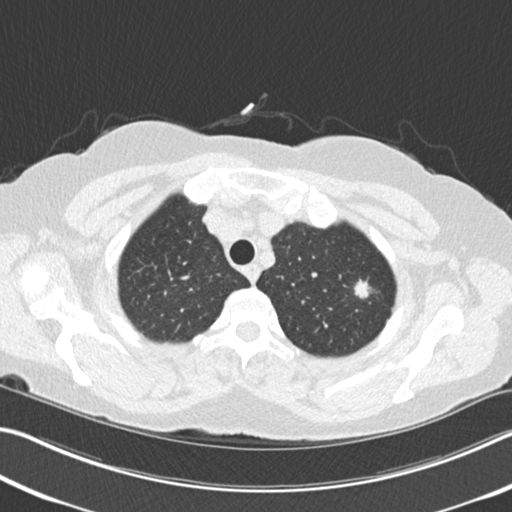
Chest CT (low-dose screening protocol), one axial image. Second annual screen. Lung window (W 1500 / L -600 HU). Standard (soft-tissue) reconstruction kernel (B30f). Slice 33 of 225 in the series. Female participant, aged 64 years at enrolment.
Expert-annotated lung lesion, bounding box <345,272,379,304> (left, top, right, bottom; pixels). Screening reader's record for this exam (one nodule recorded; not confirmed to be the boxed lesion): non-calcified nodule or mass ≥4 mm, left upper lobe, 13 × 10 mm, spiculated (stellate) margins, soft tissue attenuation, pre-existing on the prior screen: yes; interval growth: yes. Official screen result: positive, other. Later outcome: lung cancer diagnosed 106 days after this screen — signet ring cell carcinoma, right upper lobe, poorly differentiated (G3), stage IA (AJCC 6th edition), 15 mm at pathology.